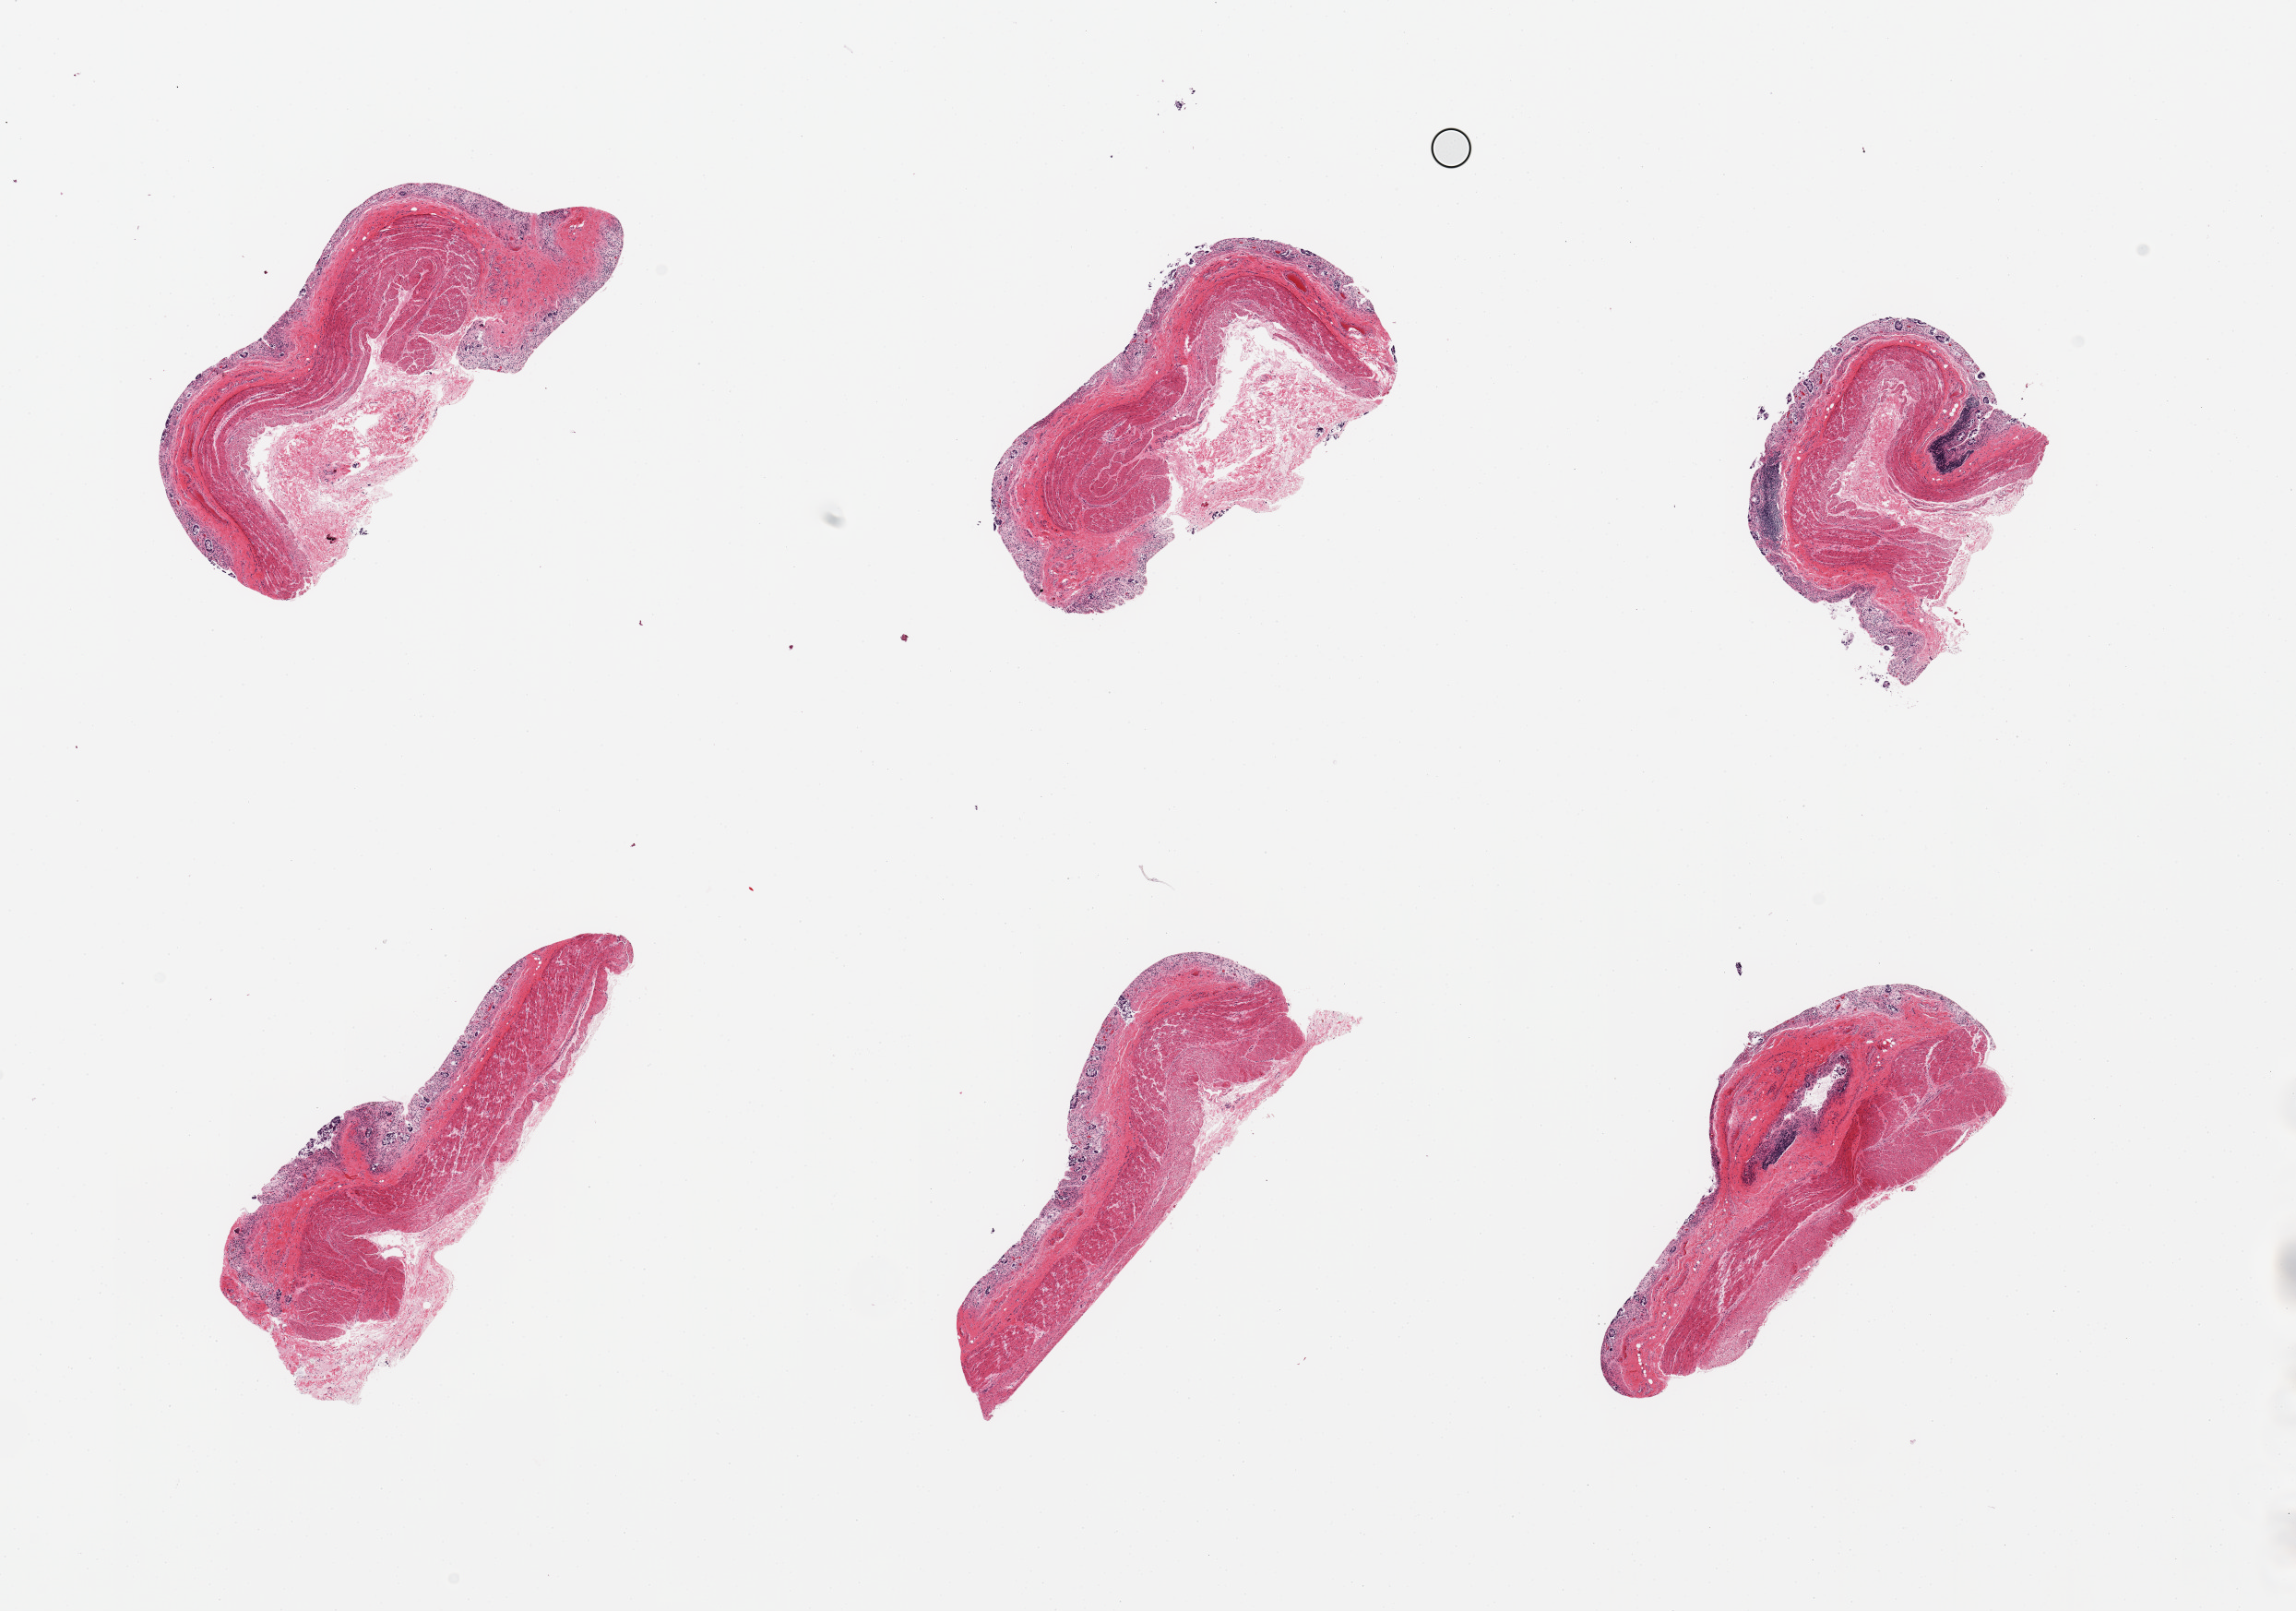
Haematoxylin and eosin whole-slide image, brightfield, whole scanned area (about 19.7 x 13.8 mm, from a 20x scan) shown as a low-resolution overview. PAXgene-fixed paraffin-embedded (PFPE) section. Section of transverse colon (target tissue). Donor tissue sample. Donor sex: female.
- pathologist's review note for this sample: 6 pieces; ; mucosa severely autolyzed, muscularis preserved